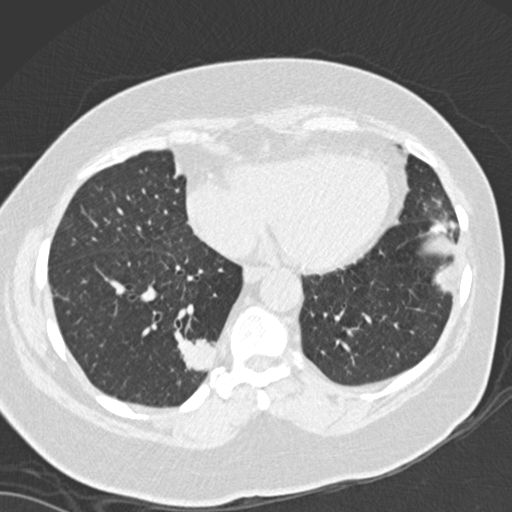
Chest CT (low-dose screening protocol), one axial image, first (baseline) screen, lung window (W 1500 / L -600 HU), slice 110 of 162 in the series. Female participant, aged 66 years at enrolment. Current smoker at enrolment.
Expert reader's lesion annotation, box from (x=143, y=312) to (x=236, y=409) px. The screening reader recorded 3 non-calcified nodules or masses ≥4 mm on this exam (left lower lobe, left lower lobe, right lower lobe); which of them this box marks is not recorded. Later outcome: lung cancer diagnosed 67 days after this screen — adenocarcinoma, NOS, right lower lobe, well differentiated (G1), stage IB (AJCC 6th edition), 55 mm at pathology.